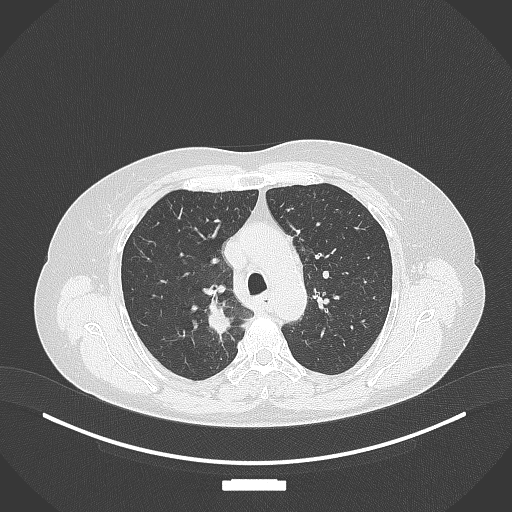
Chest CT, one axial slice. Position 273 of 357 along the scan axis. Lung window (W 1500 / L -600 HU). 1 mm slice thickness. 512 × 512 image matrix. Patient: female, 62 years. From the clinical record (not read from this slice): clinical TNM (as recorded): T1c N1 M0.
Structures marked on this image (bounding box drawn by a radiologist):
- lung tumour (recorded histology: squamous cell carcinoma): bounding box [x1, y1, x2, y2] px = [208, 298, 238, 336]